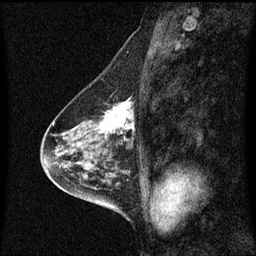
Breast MRI (dynamic contrast-enhanced), one sagittal slice. Slice 29 of 60 in the series (ordered by position). Dynamic contrast-enhanced series, image 2 of 3 at this slice position (ordered by acquisition). 1.5 T. TE 4.2 ms, TR 8.4 ms. 2 mm slice thickness. 256 × 256 image matrix, field of view 200 × 200 mm. Patient: female, 58 years.
Structures marked on this image (semi-automatic segmentation, software-assisted and operator-edited):
- analysis volume of interest (the breast-tissue region the enhancement analysis was run in; not a lesion): box from (x=86, y=98) to (x=135, y=143) px
- tumour enhancement mask (voxels above the 70 % enhancement threshold inside the analysis volume of interest): (x=99, y=100)–(x=135, y=141)